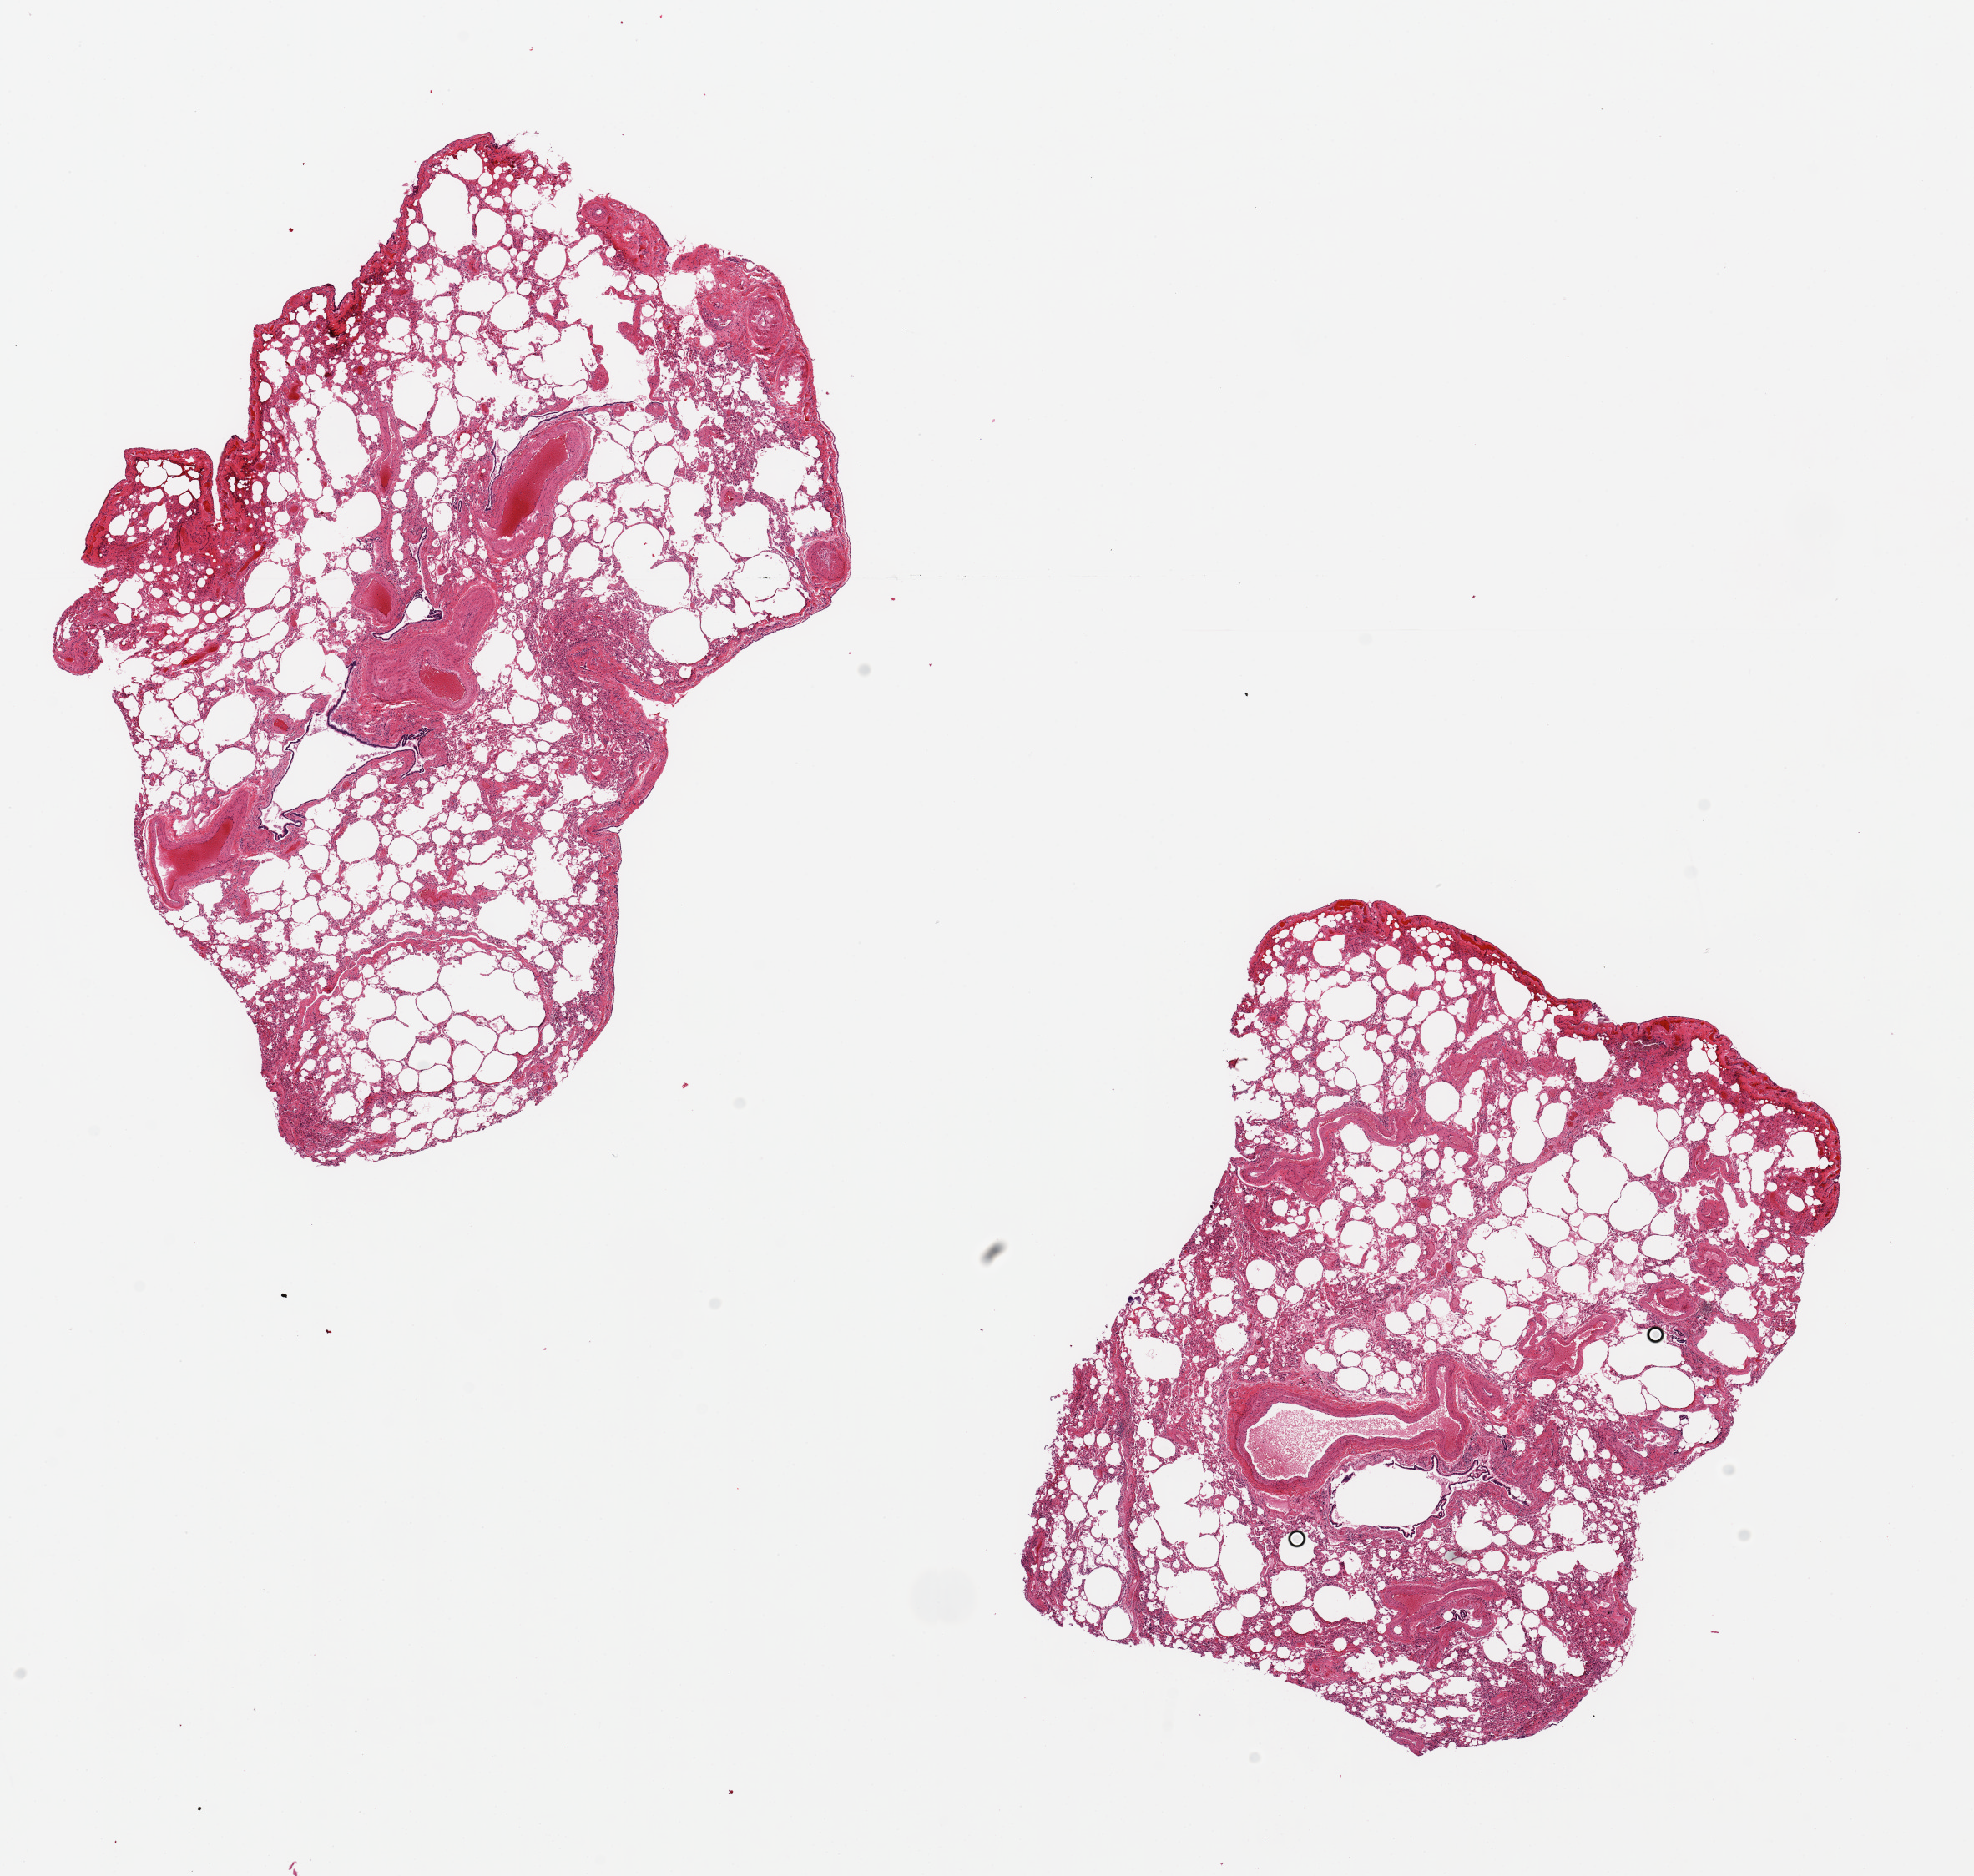
Digitized H&E-stained section, shown as a low-resolution overview of the whole scanned area (about 18.7 x 17.8 mm), PAXgene-fixed paraffin-embedded (PFPE) section, sampled site (target tissue): lung, tissue donor sample.
Pathologist's review note for this sample: 2 pieces, 9x7 & 8x6mm.